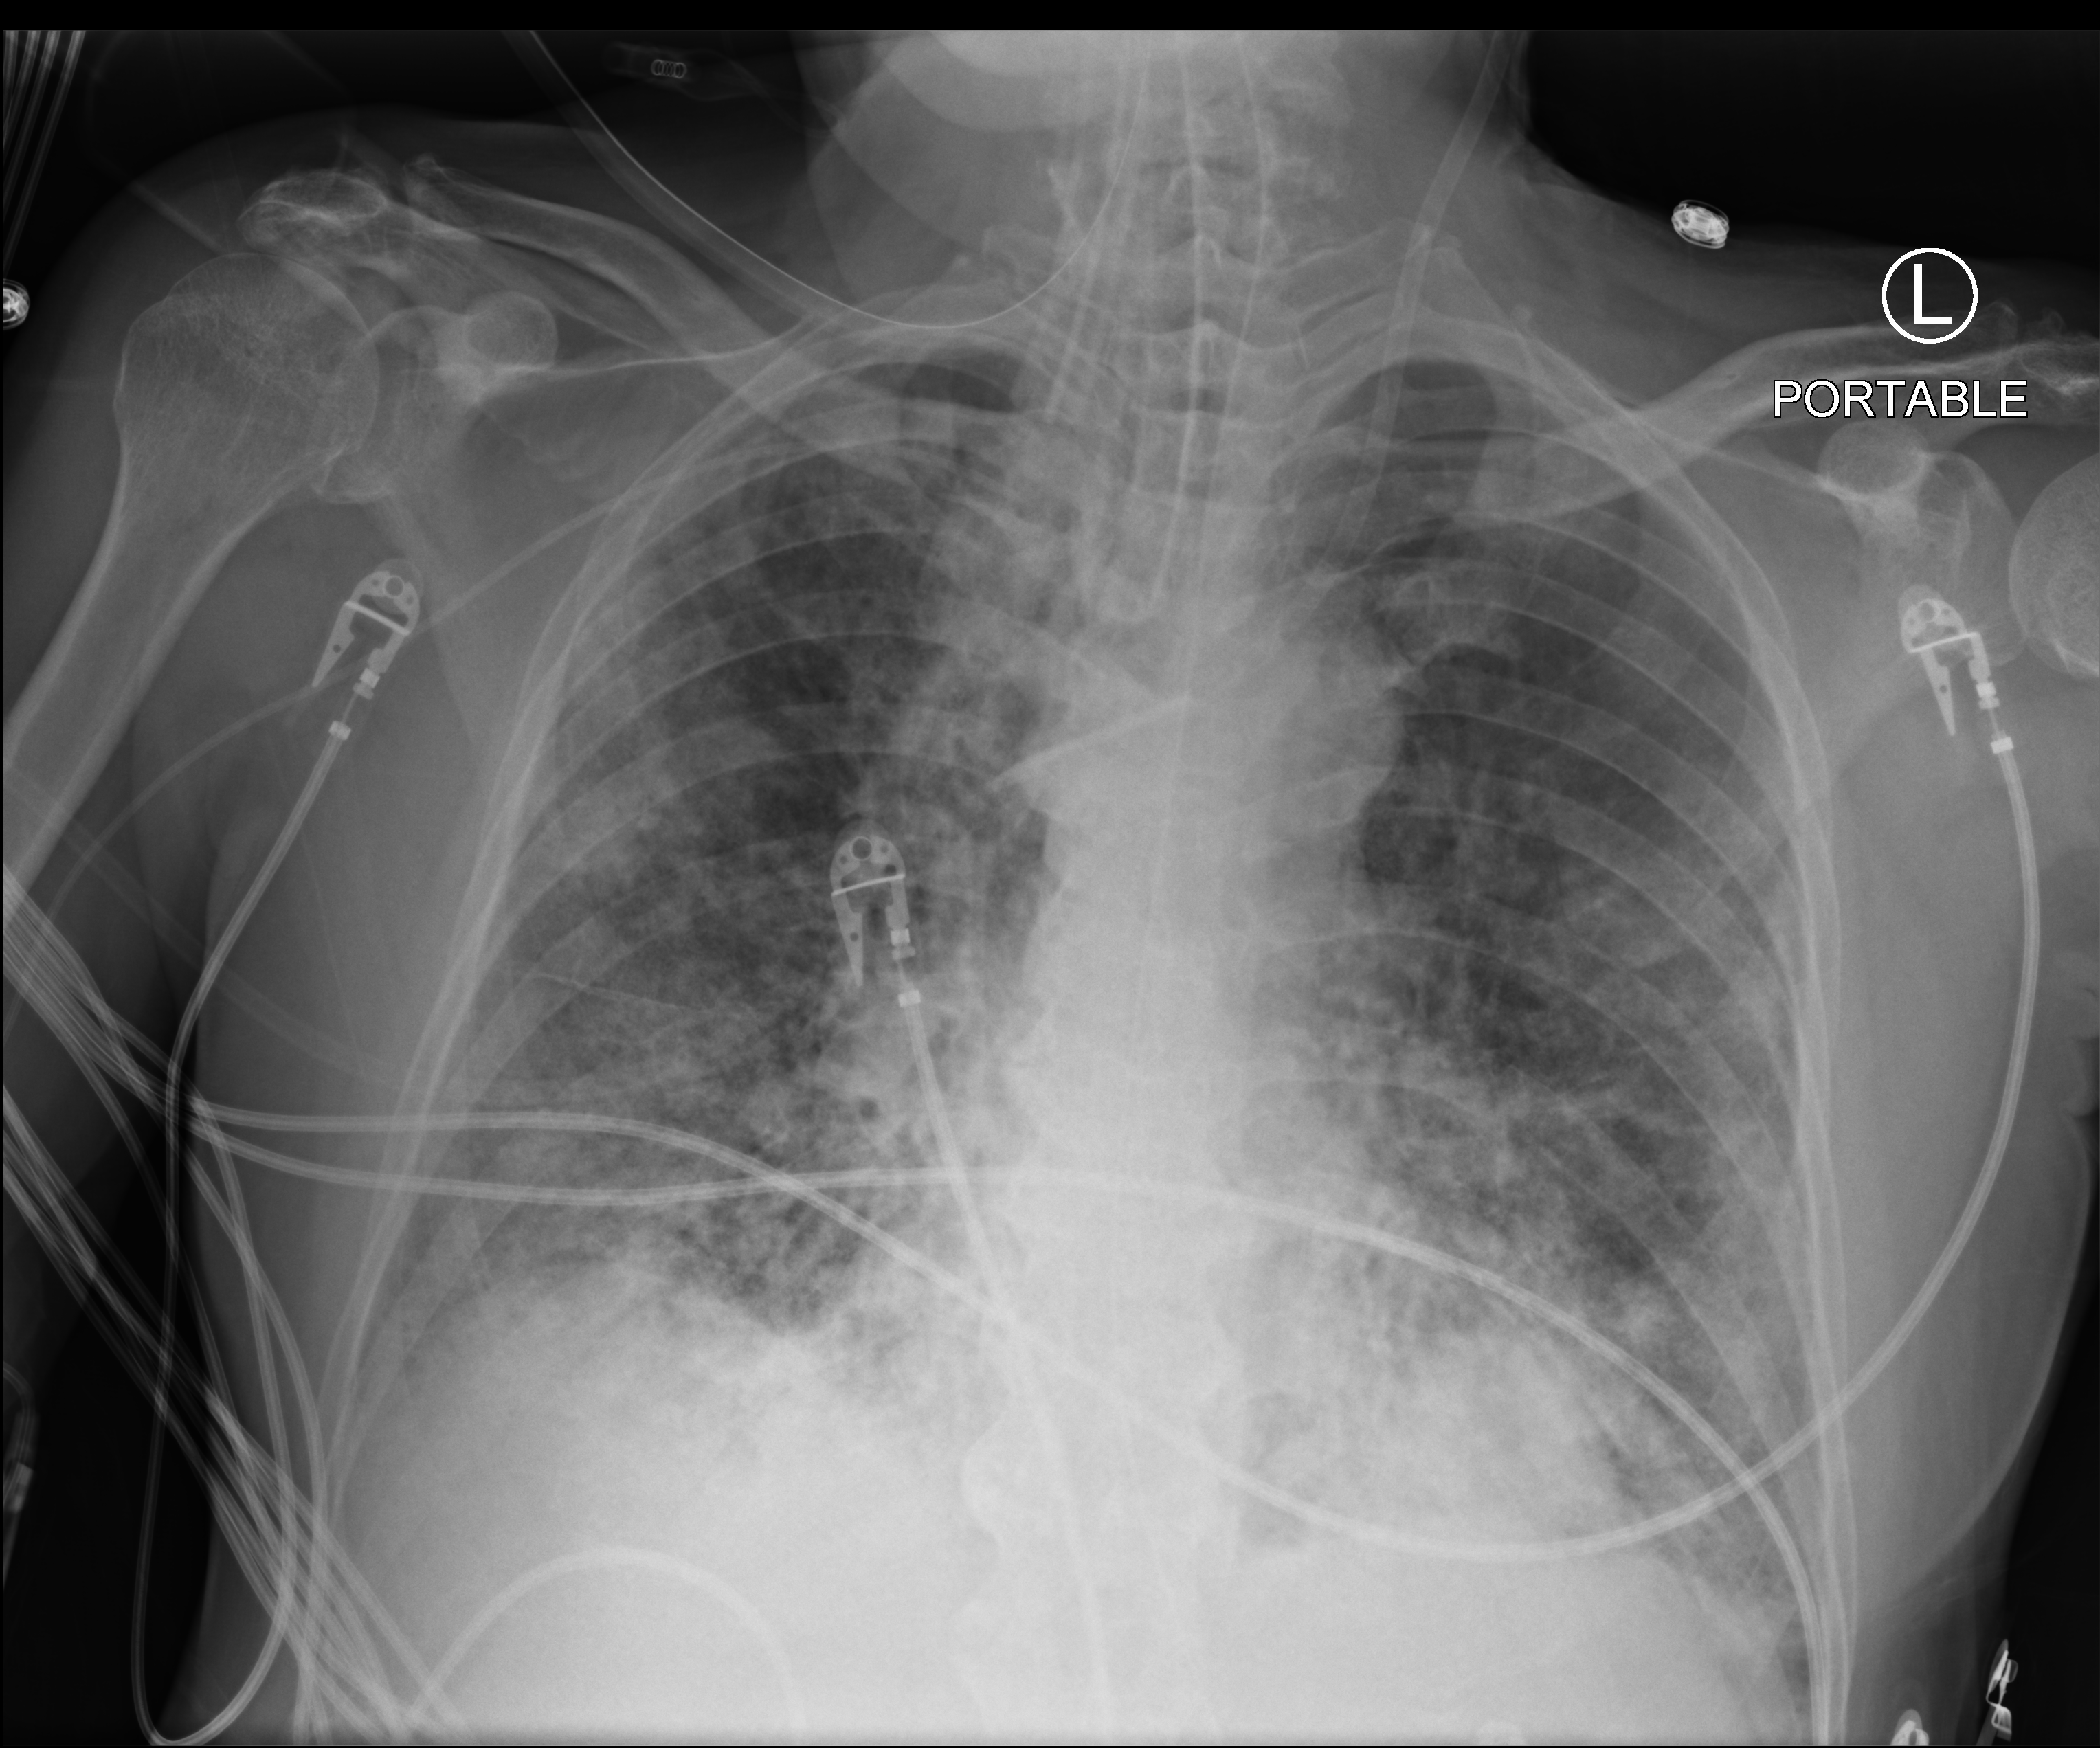
Bedside chest radiograph (computed radiography); anteroposterior (AP) projection. Patient hospitalised with COVID-19; male, aged 60–74 years.
Admission-level facts for this patient (not findings on this image; timing relative to this image not recorded):
- mechanically ventilated during this hospital stay: yes